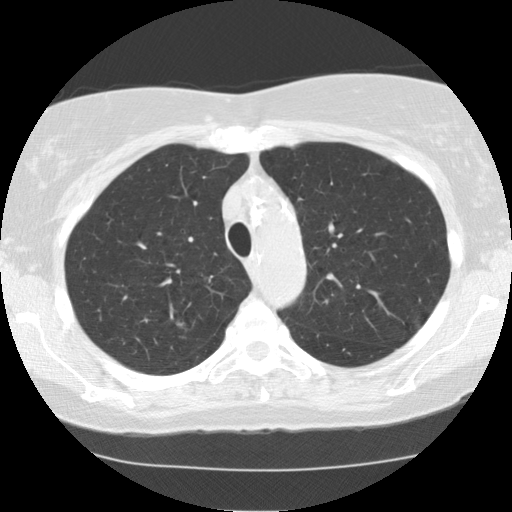
Low-dose screening chest CT, axial slice. Baseline annual screen. Lung window (W 1500 / L -600 HU). 2.5 mm slice thickness. Standard (soft-tissue) reconstruction kernel (STANDARD). 120 kVp. 512 × 512 image matrix, field of view 326 × 326 mm. Female, age 72 years at enrolment. Former smoker at enrolment.
- Expert-annotated lung lesion, bounding box [x1, y1, x2, y2] px = [165, 302, 203, 344].
- The screening reader recorded 5 non-calcified nodules or masses ≥4 mm on this exam (right upper lobe, right upper lobe, right upper lobe, right upper lobe, right lower lobe); which of them this box marks is not recorded.
- Lung cancer was diagnosed 812 days after this screen (after the third annual screen): bronchiolo-alveolar adenocarcinoma, NOS, right upper lobe, well differentiated (G1), stage IA (AJCC 6th edition), 8 mm at pathology.